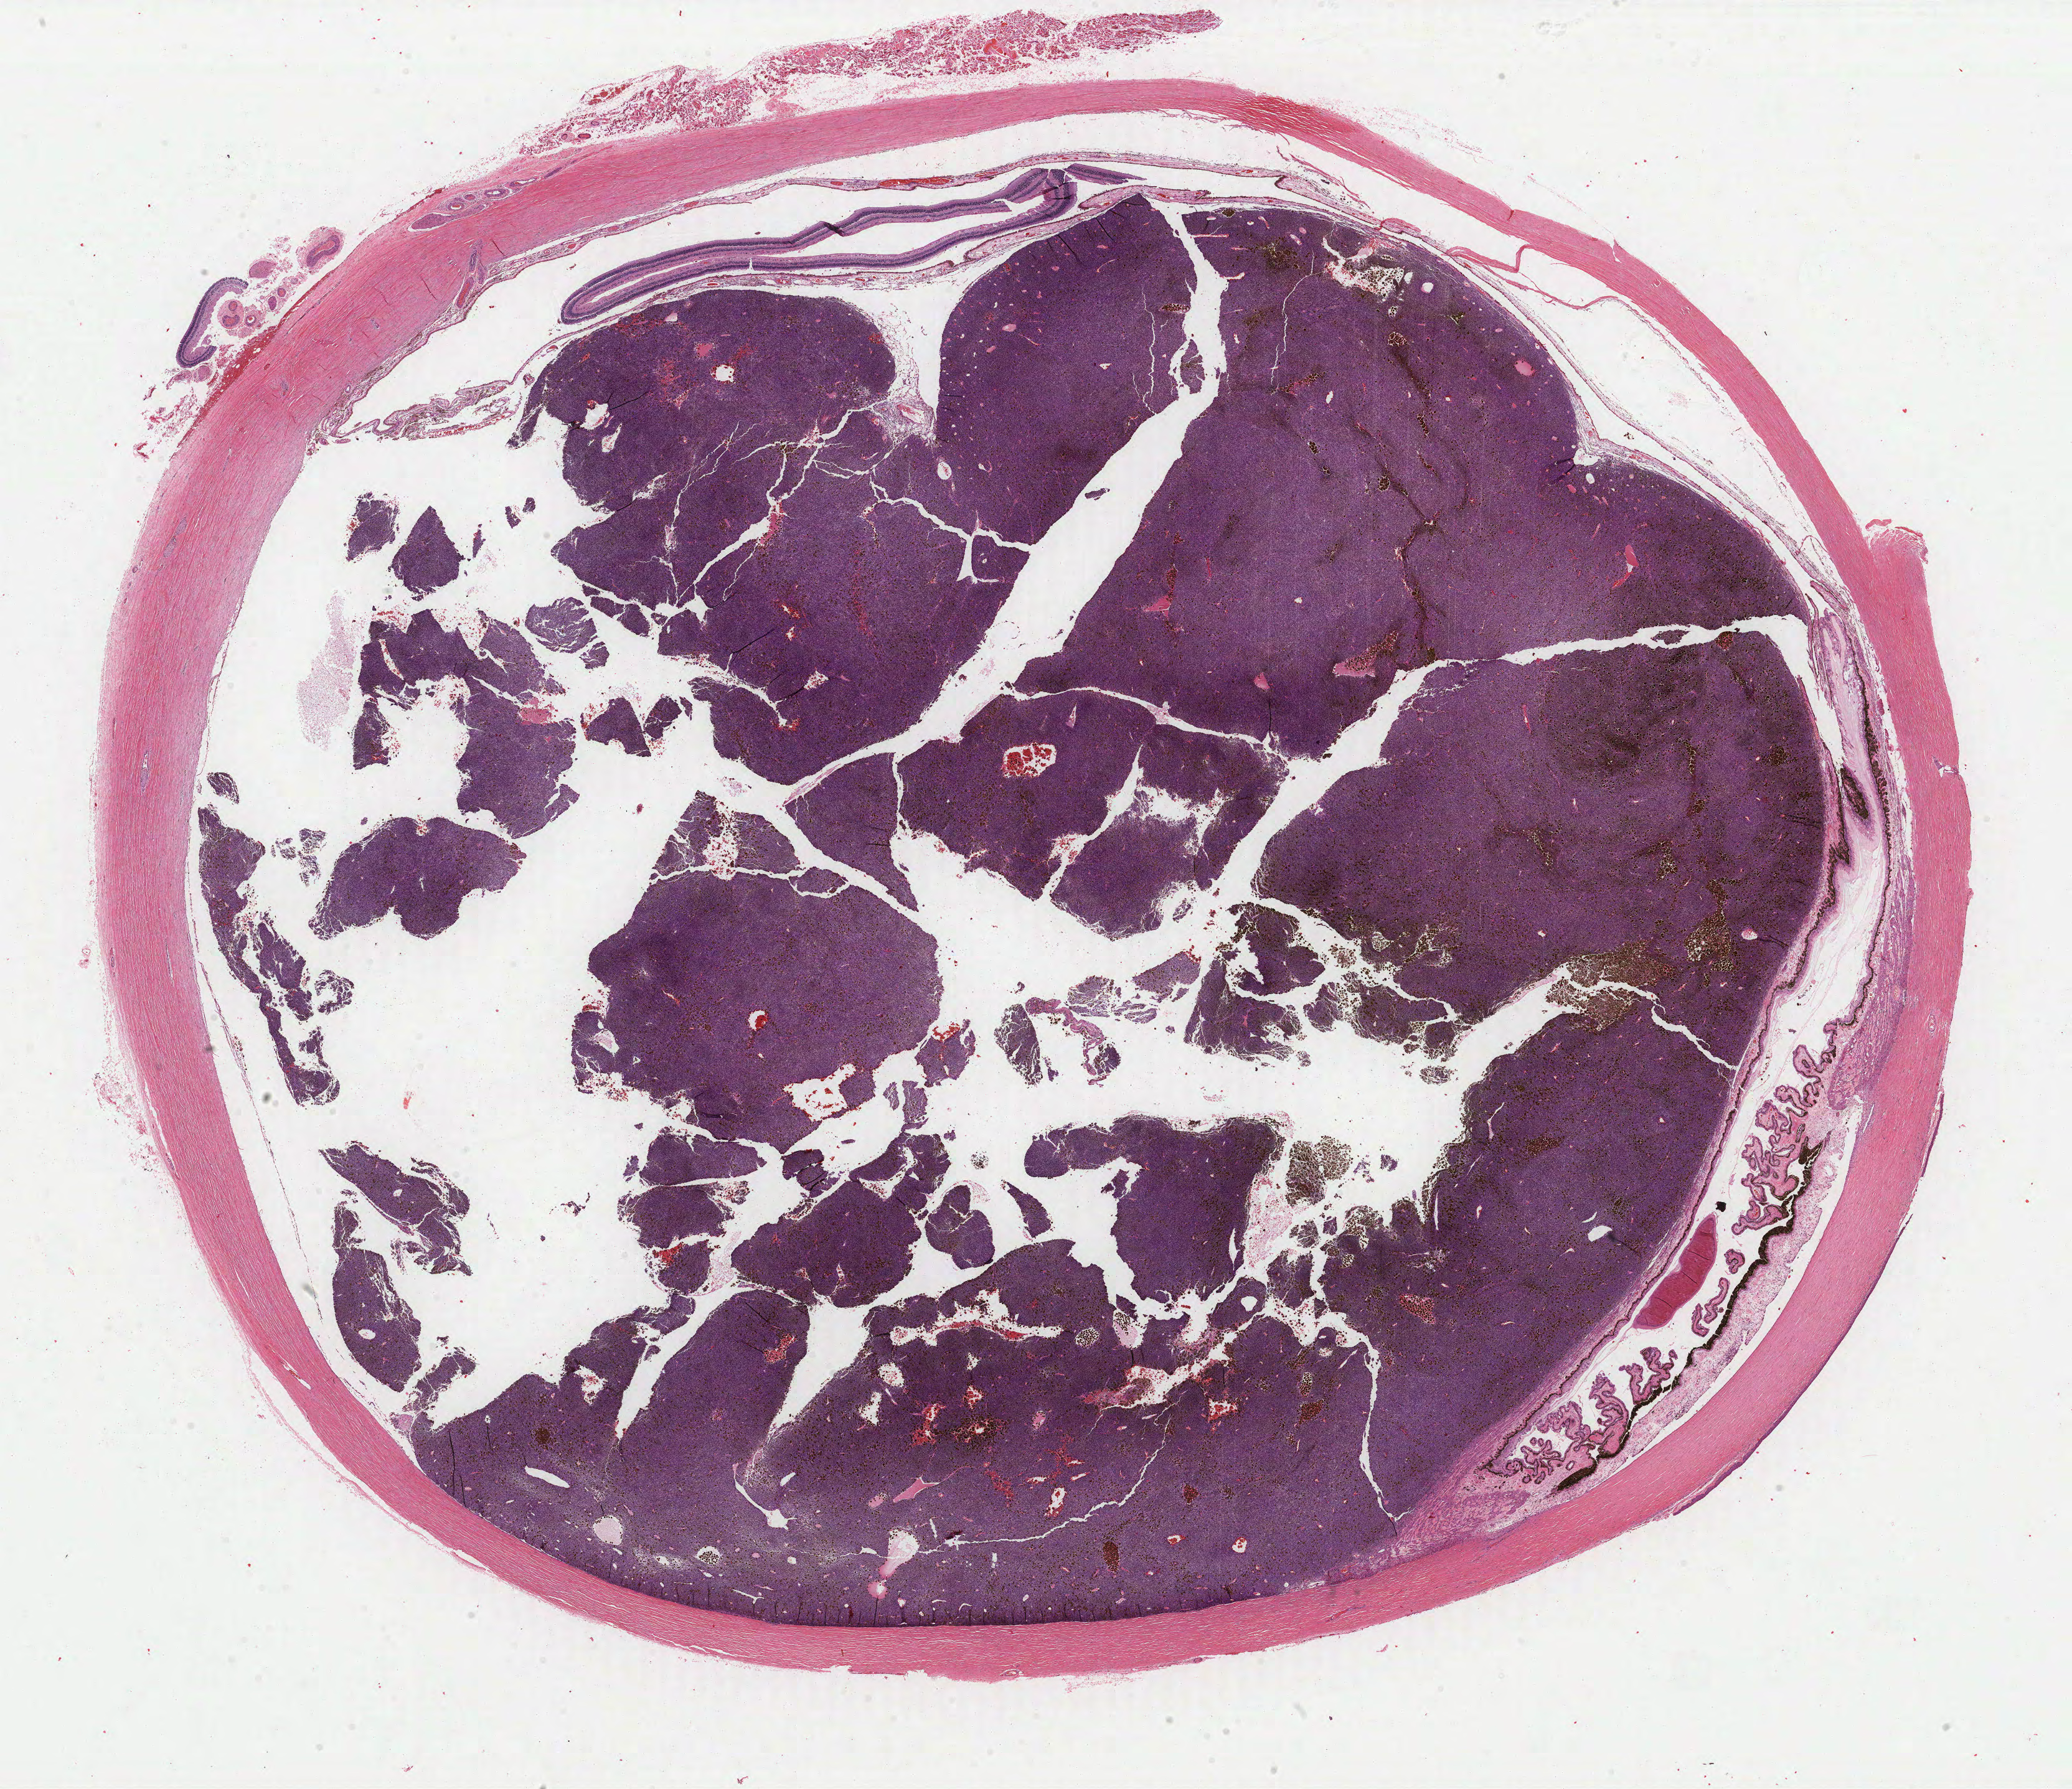
H&E whole-slide image — low-resolution overview of the scanned area, about 26.3 x 22.7 mm (acquisition: 40x scan). Formalin-fixed paraffin-embedded (FFPE) diagnostic section. Uvea, primary tumour sample. Patient: female, age at initial diagnosis 79 years.
Diagnosis: Spindle cell melanoma, NOS (eye, NOS).